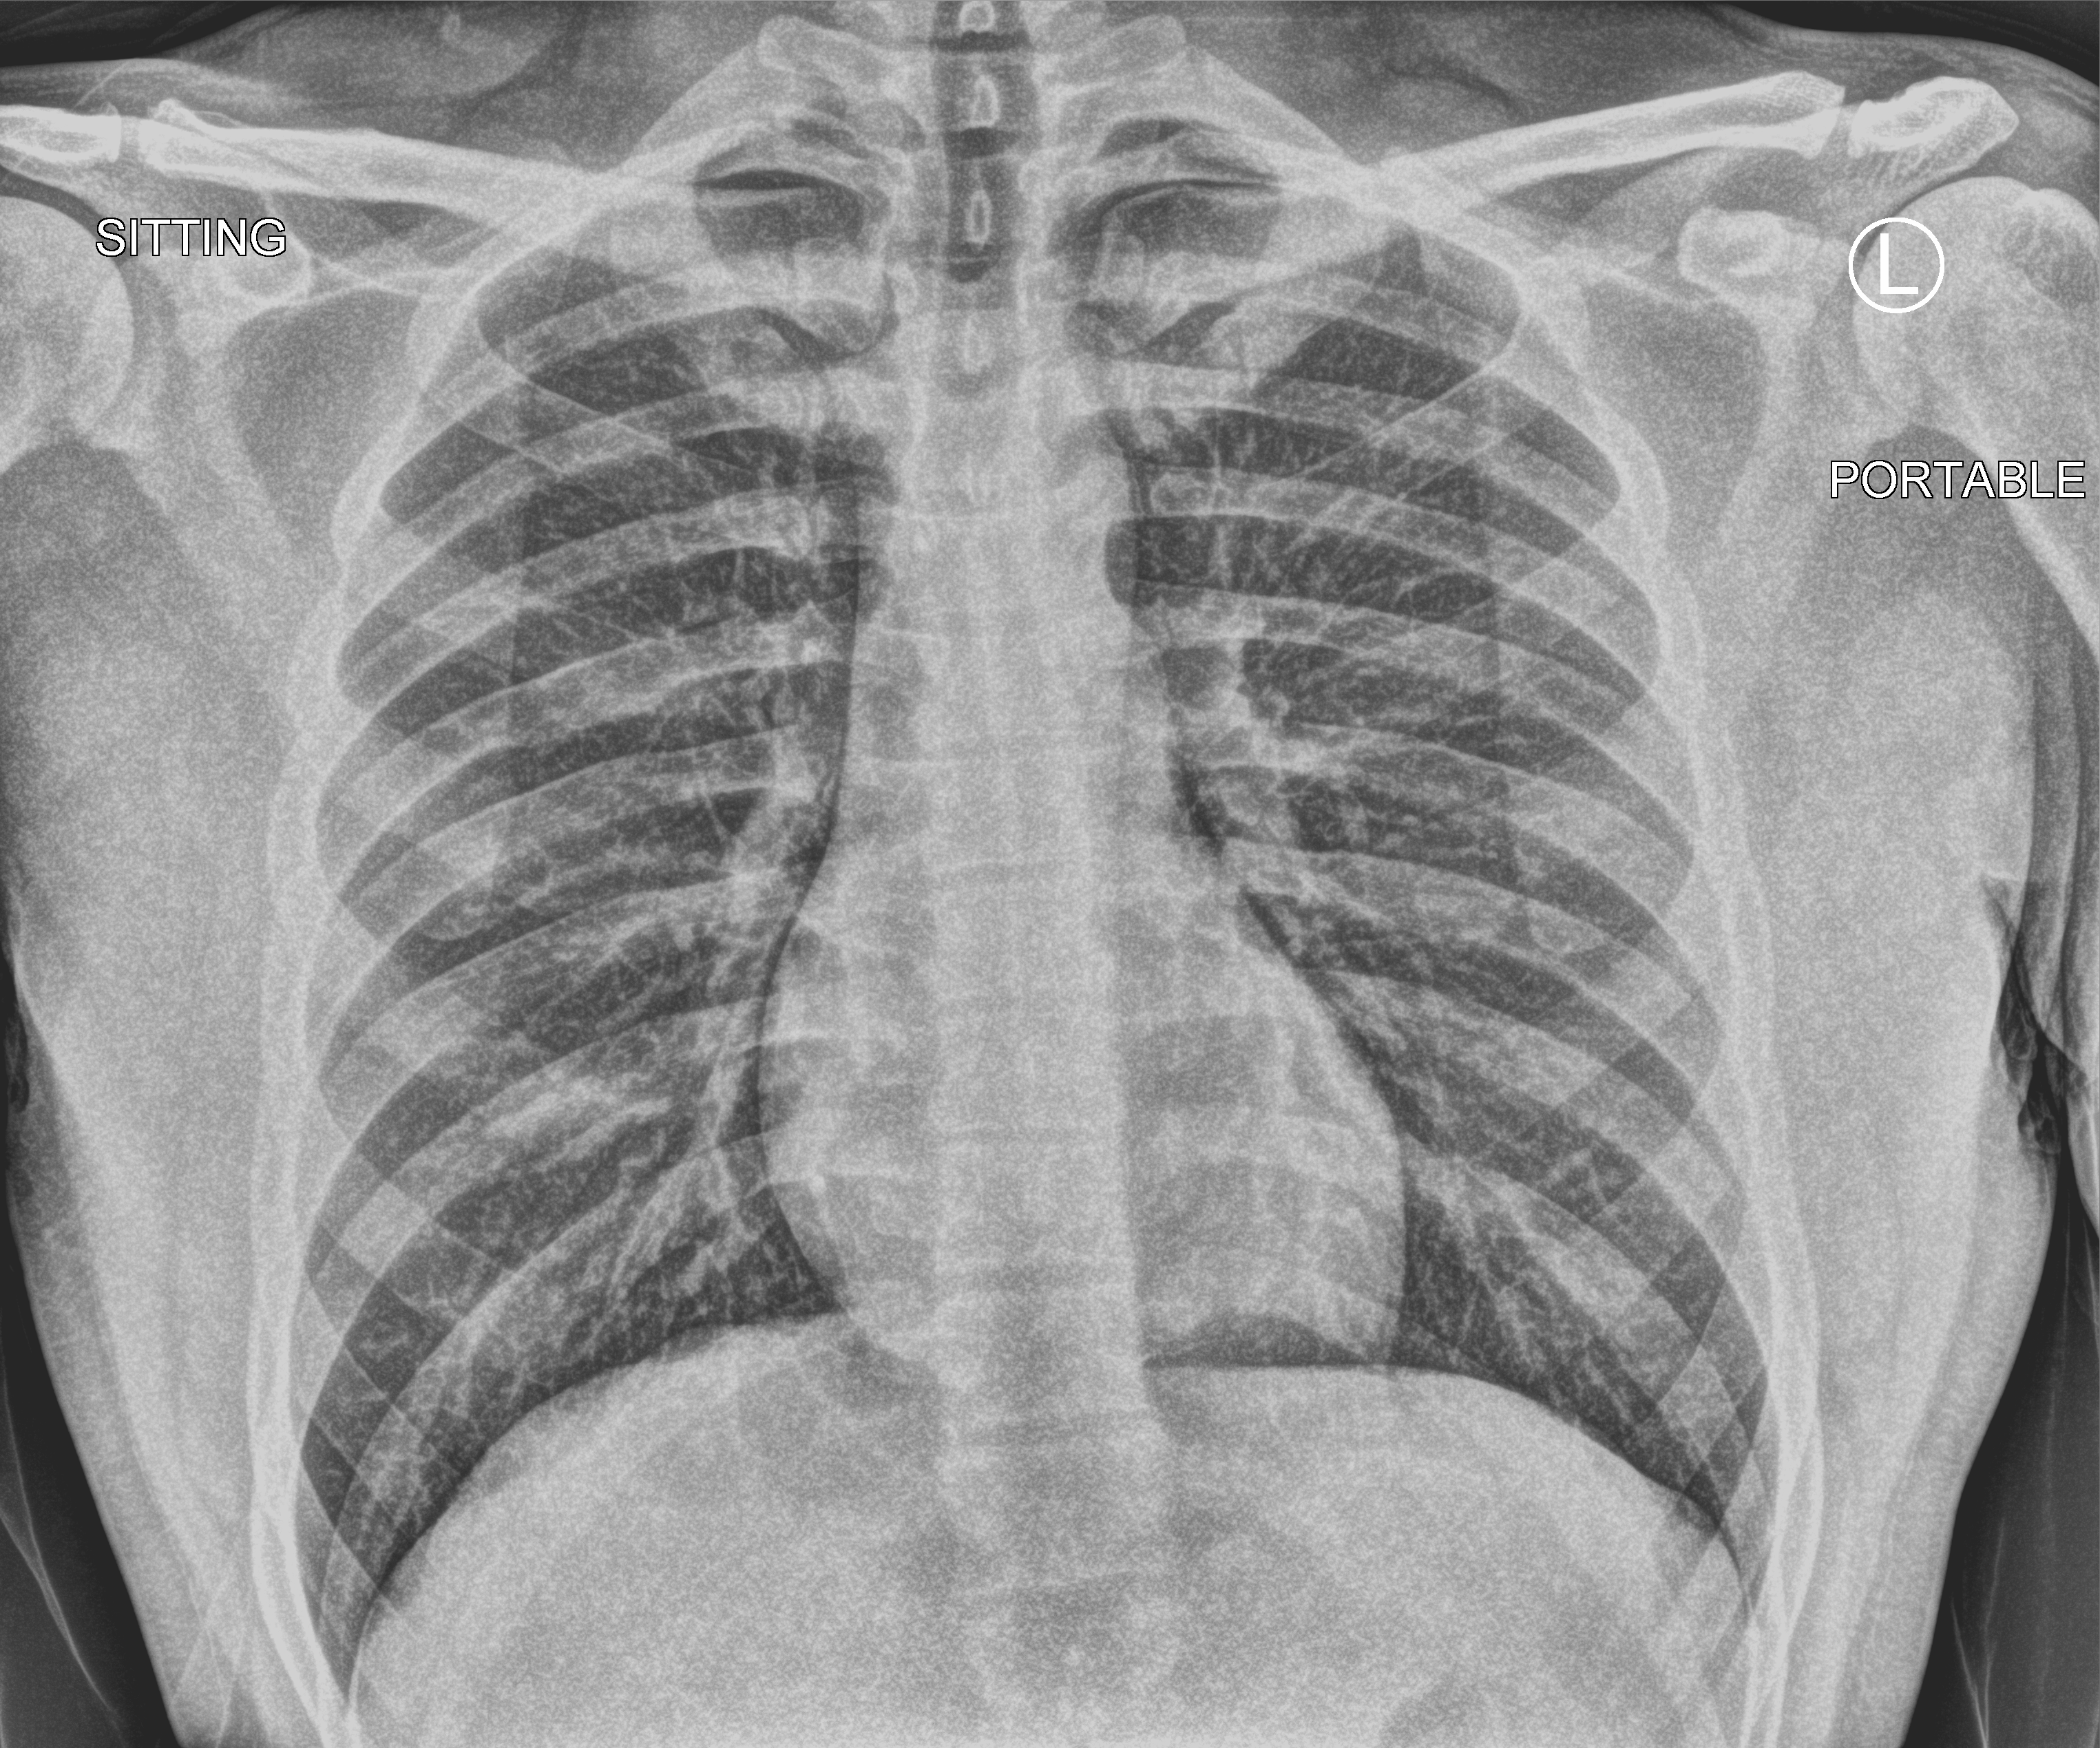
Bedside chest radiograph (computed radiography); anteroposterior (AP) projection. Male patient hospitalised with COVID-19, age 18–59 years.
Admission-level facts for this patient (not findings on this image; timing relative to this image not recorded): mechanically ventilated during this hospital stay: no; other chronic lung disease (admission record): yes.